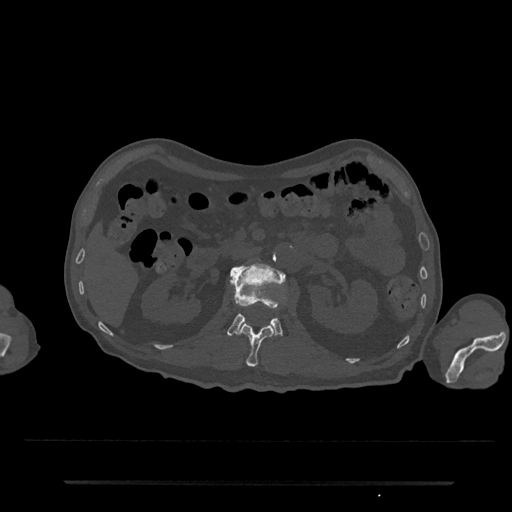
CT including the spine, one axial slice. Slice 98 of 797 in the series (ordered by position). Reconstruction kernel Br40s/3. Bone window (W 1800 / L 400 HU). 0.5 mm slice thickness. 512 × 512 image matrix, field of view 427 × 427 mm. Patient: male, 74 years. From the clinical record (not read from this slice): primary cancer: prostate.
Annotated regions visible in this slice (semi-automatic segmentation, software-assisted and operator-edited):
- L1 vertebra: bounding box (x1, y1, x2, y2) in pixels: (237, 322, 274, 367)
- L2 vertebra: (227, 262, 284, 336)